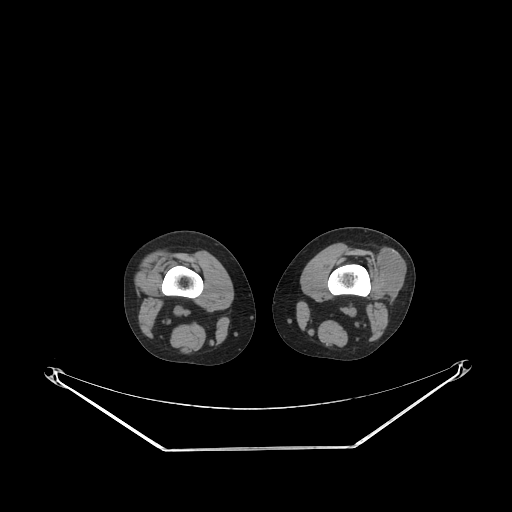
CT of an extremity soft-tissue mass (from a PET/CT study), one axial slice. Slice 175 of 223 in the series (ordered by position). Reconstruction kernel STANDARD. 140 kVp. Soft-tissue window (W 400 / L 40 HU). 3.75 mm slice thickness. 512 × 512 image matrix. Female patient. From the clinical record (not read from this slice): histological type: spindle cell suggestive of biphasic synovial sarcoma; grade: intermediate; site of the primary tumour: left knee.
Annotated regions visible in this slice (expert contour drawn on MRI and transferred to this co-registered scan by the dataset authors):
- gross tumour volume including surrounding oedema: bounding box [x1, y1, x2, y2] px = [374, 244, 403, 296]
- gross tumour volume (mass): [375, 247, 403, 296]